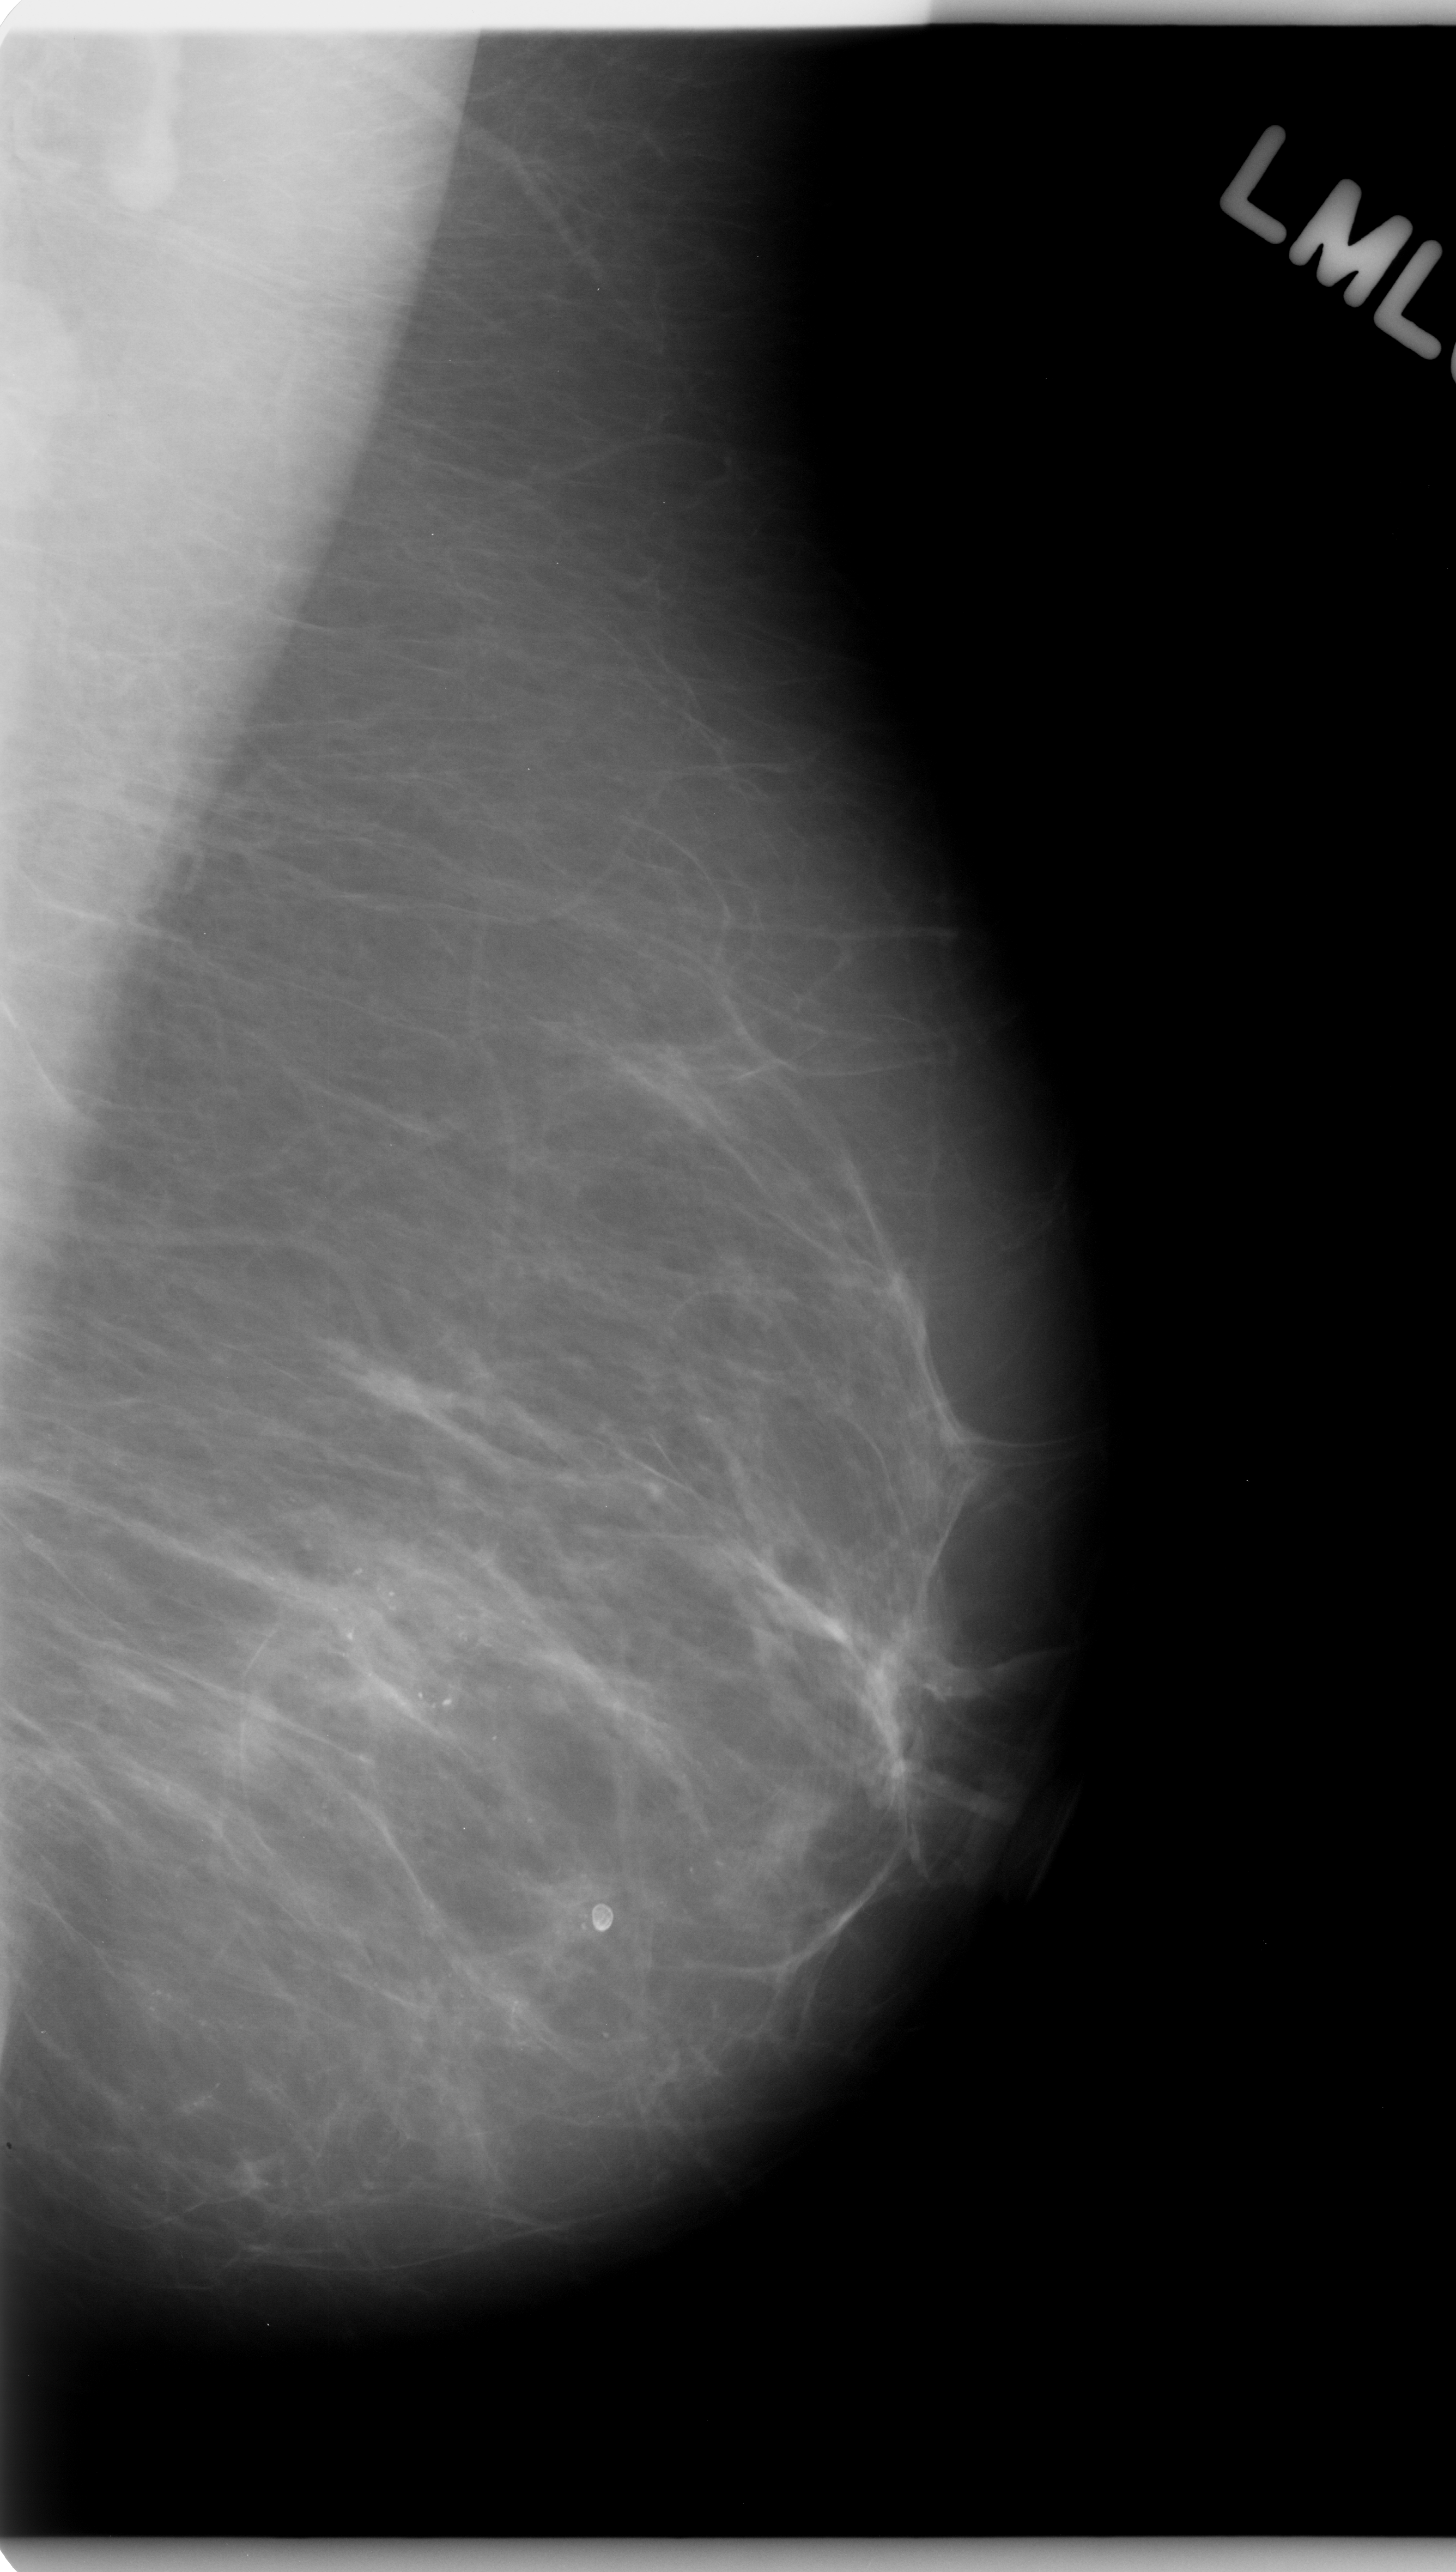
Mammogram (digitized film). Left breast. MLO view. BI-RADS breast density category 1 (scale 1–4). 1456 × 2572 image matrix.
Expert-marked regions of interest on this image (one box per marked abnormality):
- calcifications, morphology amorphous, distribution regional; BI-RADS assessment category 5; pathology result (as recorded, not read from the image): malignant: bounding box (x1, y1, x2, y2) in pixels: (4, 1364, 829, 2181)